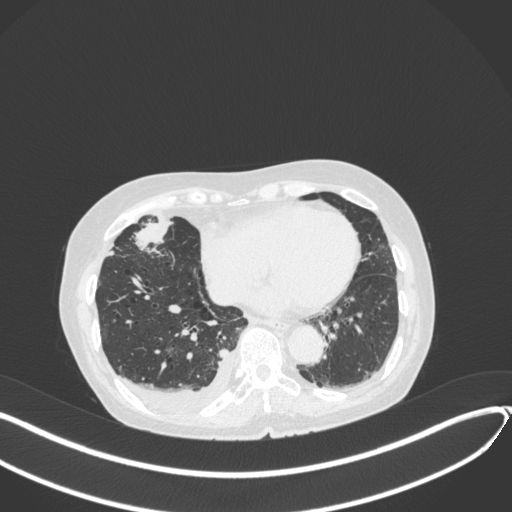
Chest CT, one axial slice; position 127 of 418 along the scan axis; reconstruction kernel B31f; lung window (W 1500 / L -600 HU); 512 × 512 image matrix, field of view 400 × 400 mm. Patient: female, 75 years. Case-level facts recorded for this patient, not image findings: clinical TNM (as recorded): T2a N3 M0.
Outlined on this slice (bounding box drawn by a radiologist):
- lung tumour (recorded histology: adenocarcinoma): box from (x=130, y=215) to (x=177, y=257) px